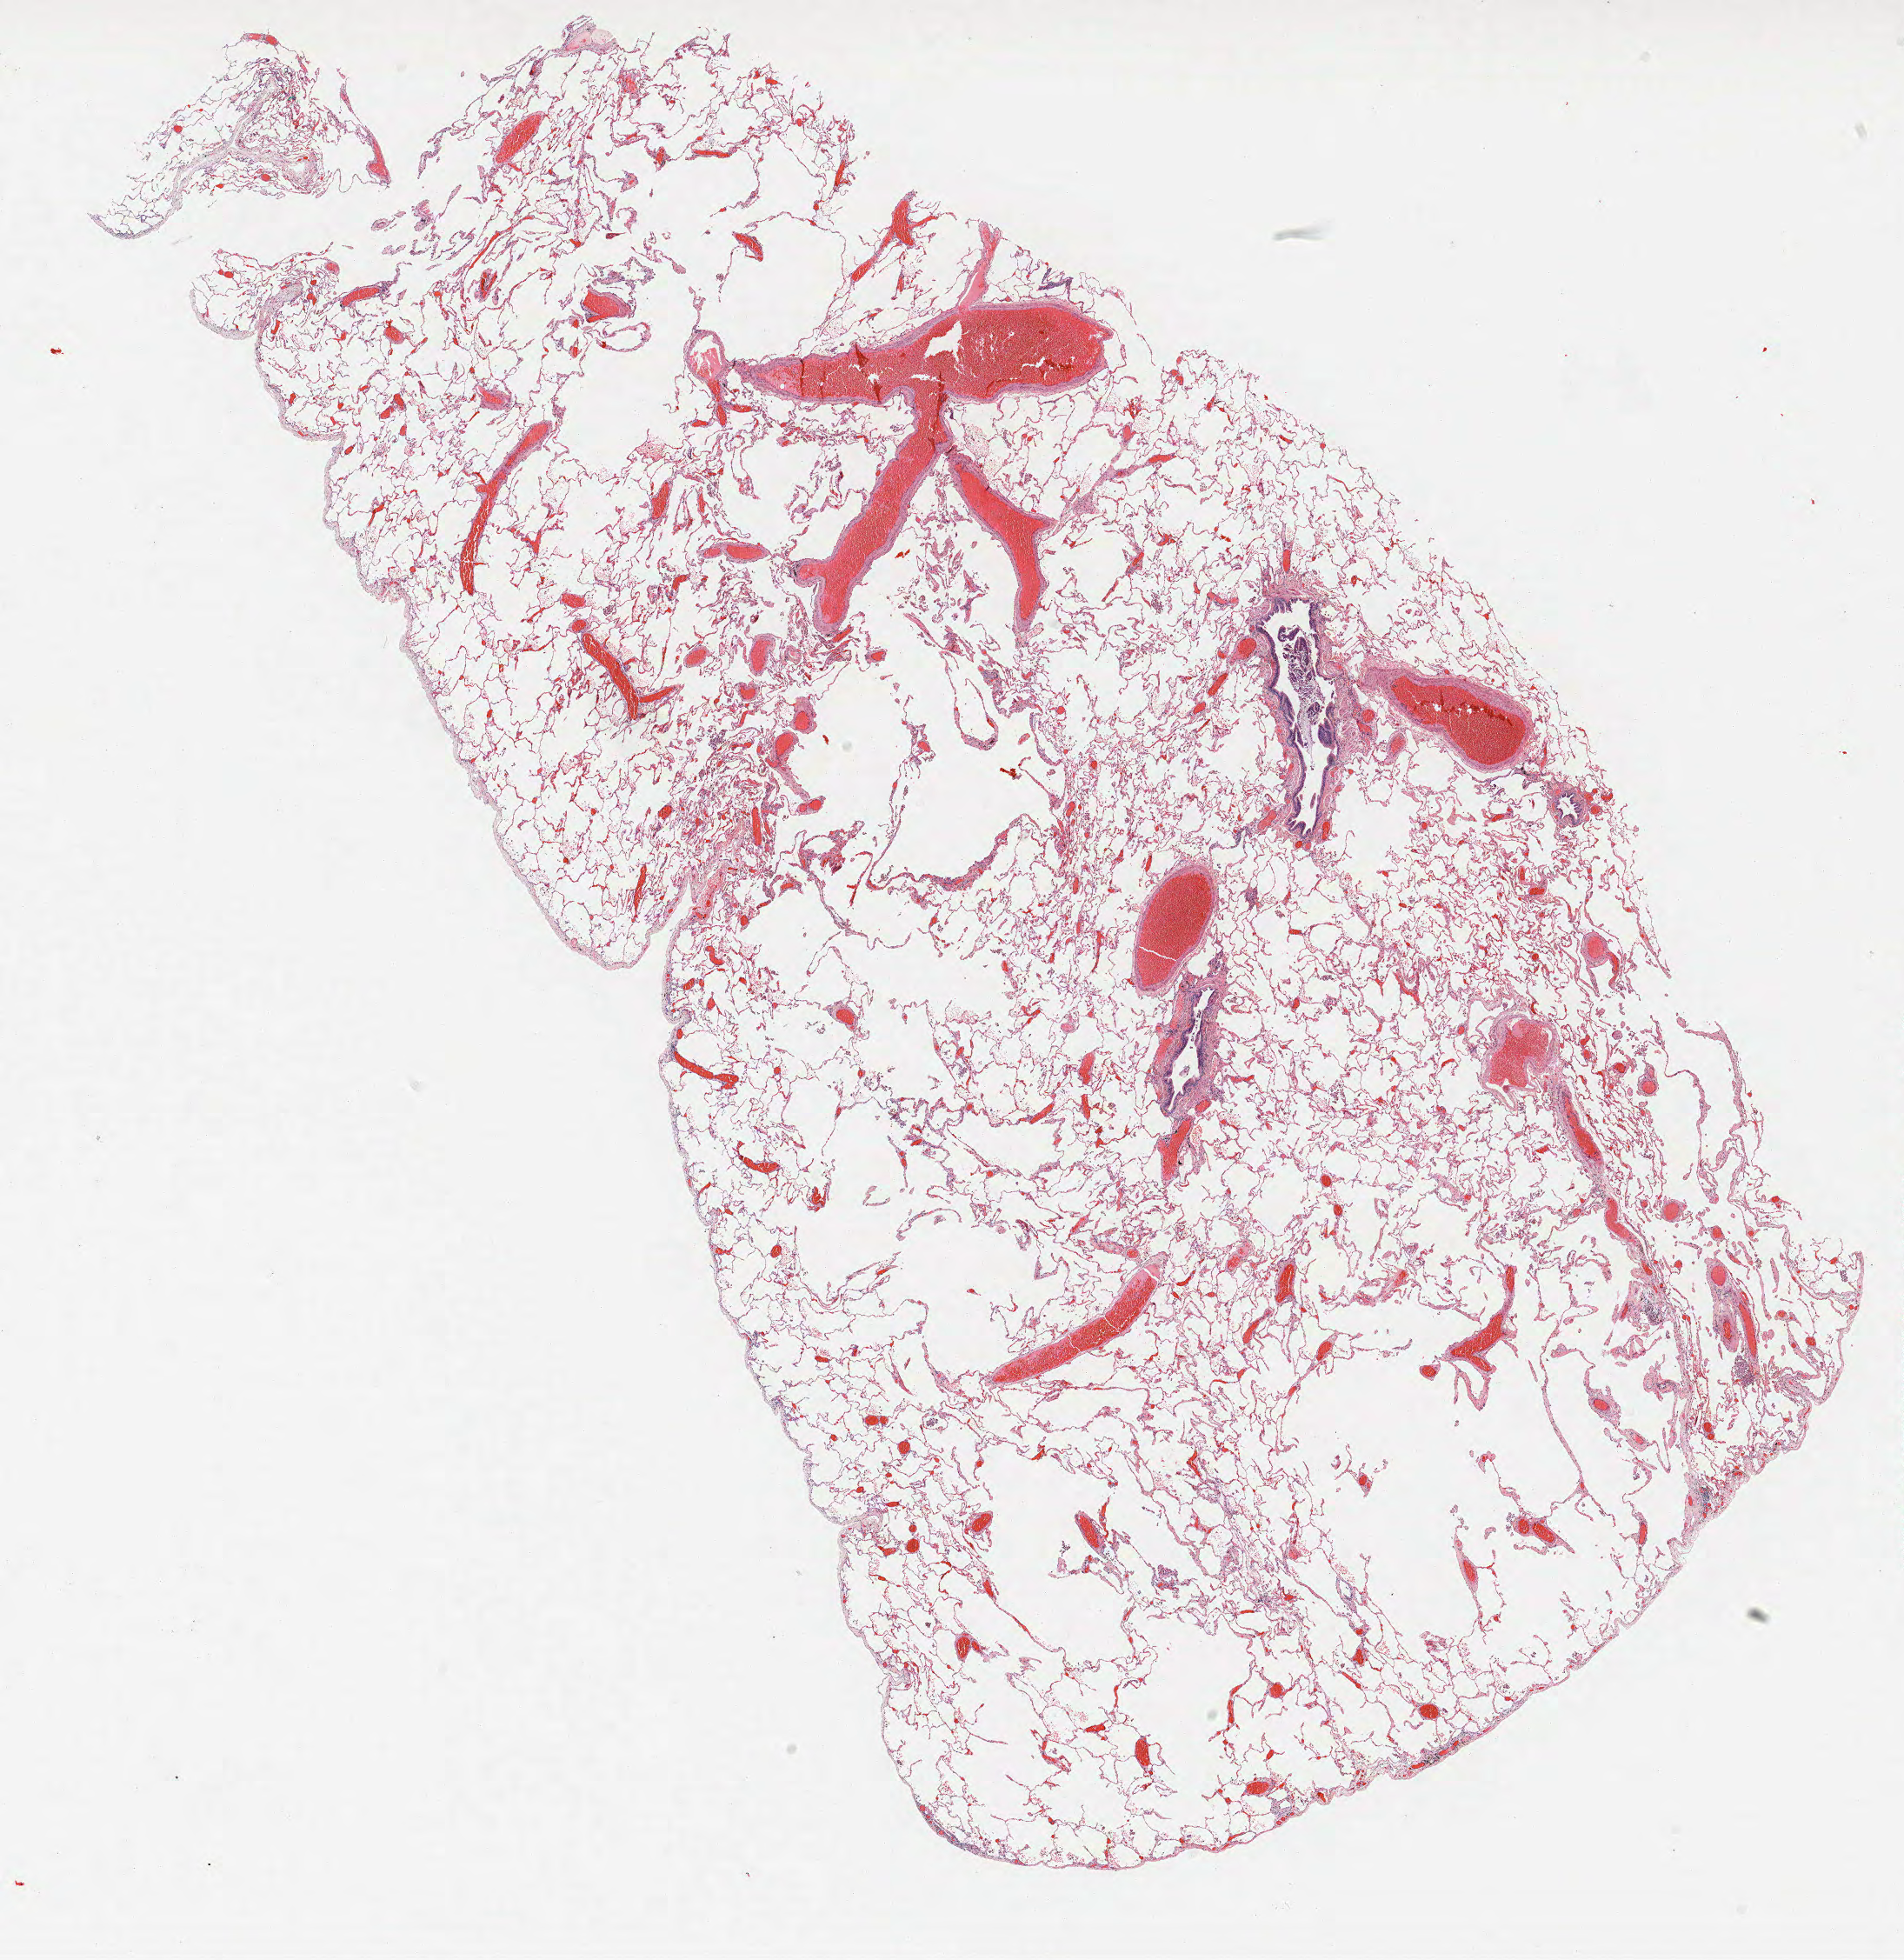
Whole-slide histology image, H&E-stained — a low-resolution overview of the entire scanned area, about 17.5 x 18.0 mm, FFPE section, lung. Female patient, aged 61 at enrolment. Grade: poorly differentiated (G3).
Stage (AJCC 6th edition): IB. Participant's lung-cancer diagnosis: Non-small cell carcinoma. Primary tumour location (clinical record): left lower lobe. Tumour size (pathology): 100 mm.